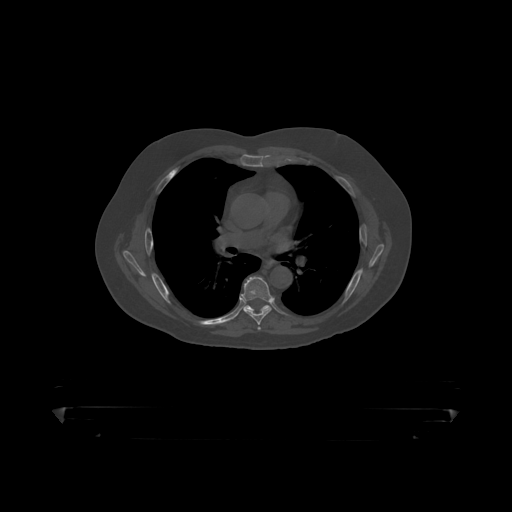
CT including the spine, one axial slice. Position 294 of 390 along the scan axis. Bone window (W 1800 / L 400 HU). 1.25 mm slice thickness. 512 × 512 image matrix, field of view 650 × 650 mm. Patient: male, 60 years. From the clinical record (not read from this slice): primary cancer: prostate.
Outlined on this slice (semi-automatically segmented with operator editing):
- T6 vertebra: box from (x=241, y=277) to (x=273, y=319) px
- T7 vertebra: (x=244, y=305)–(x=271, y=311)